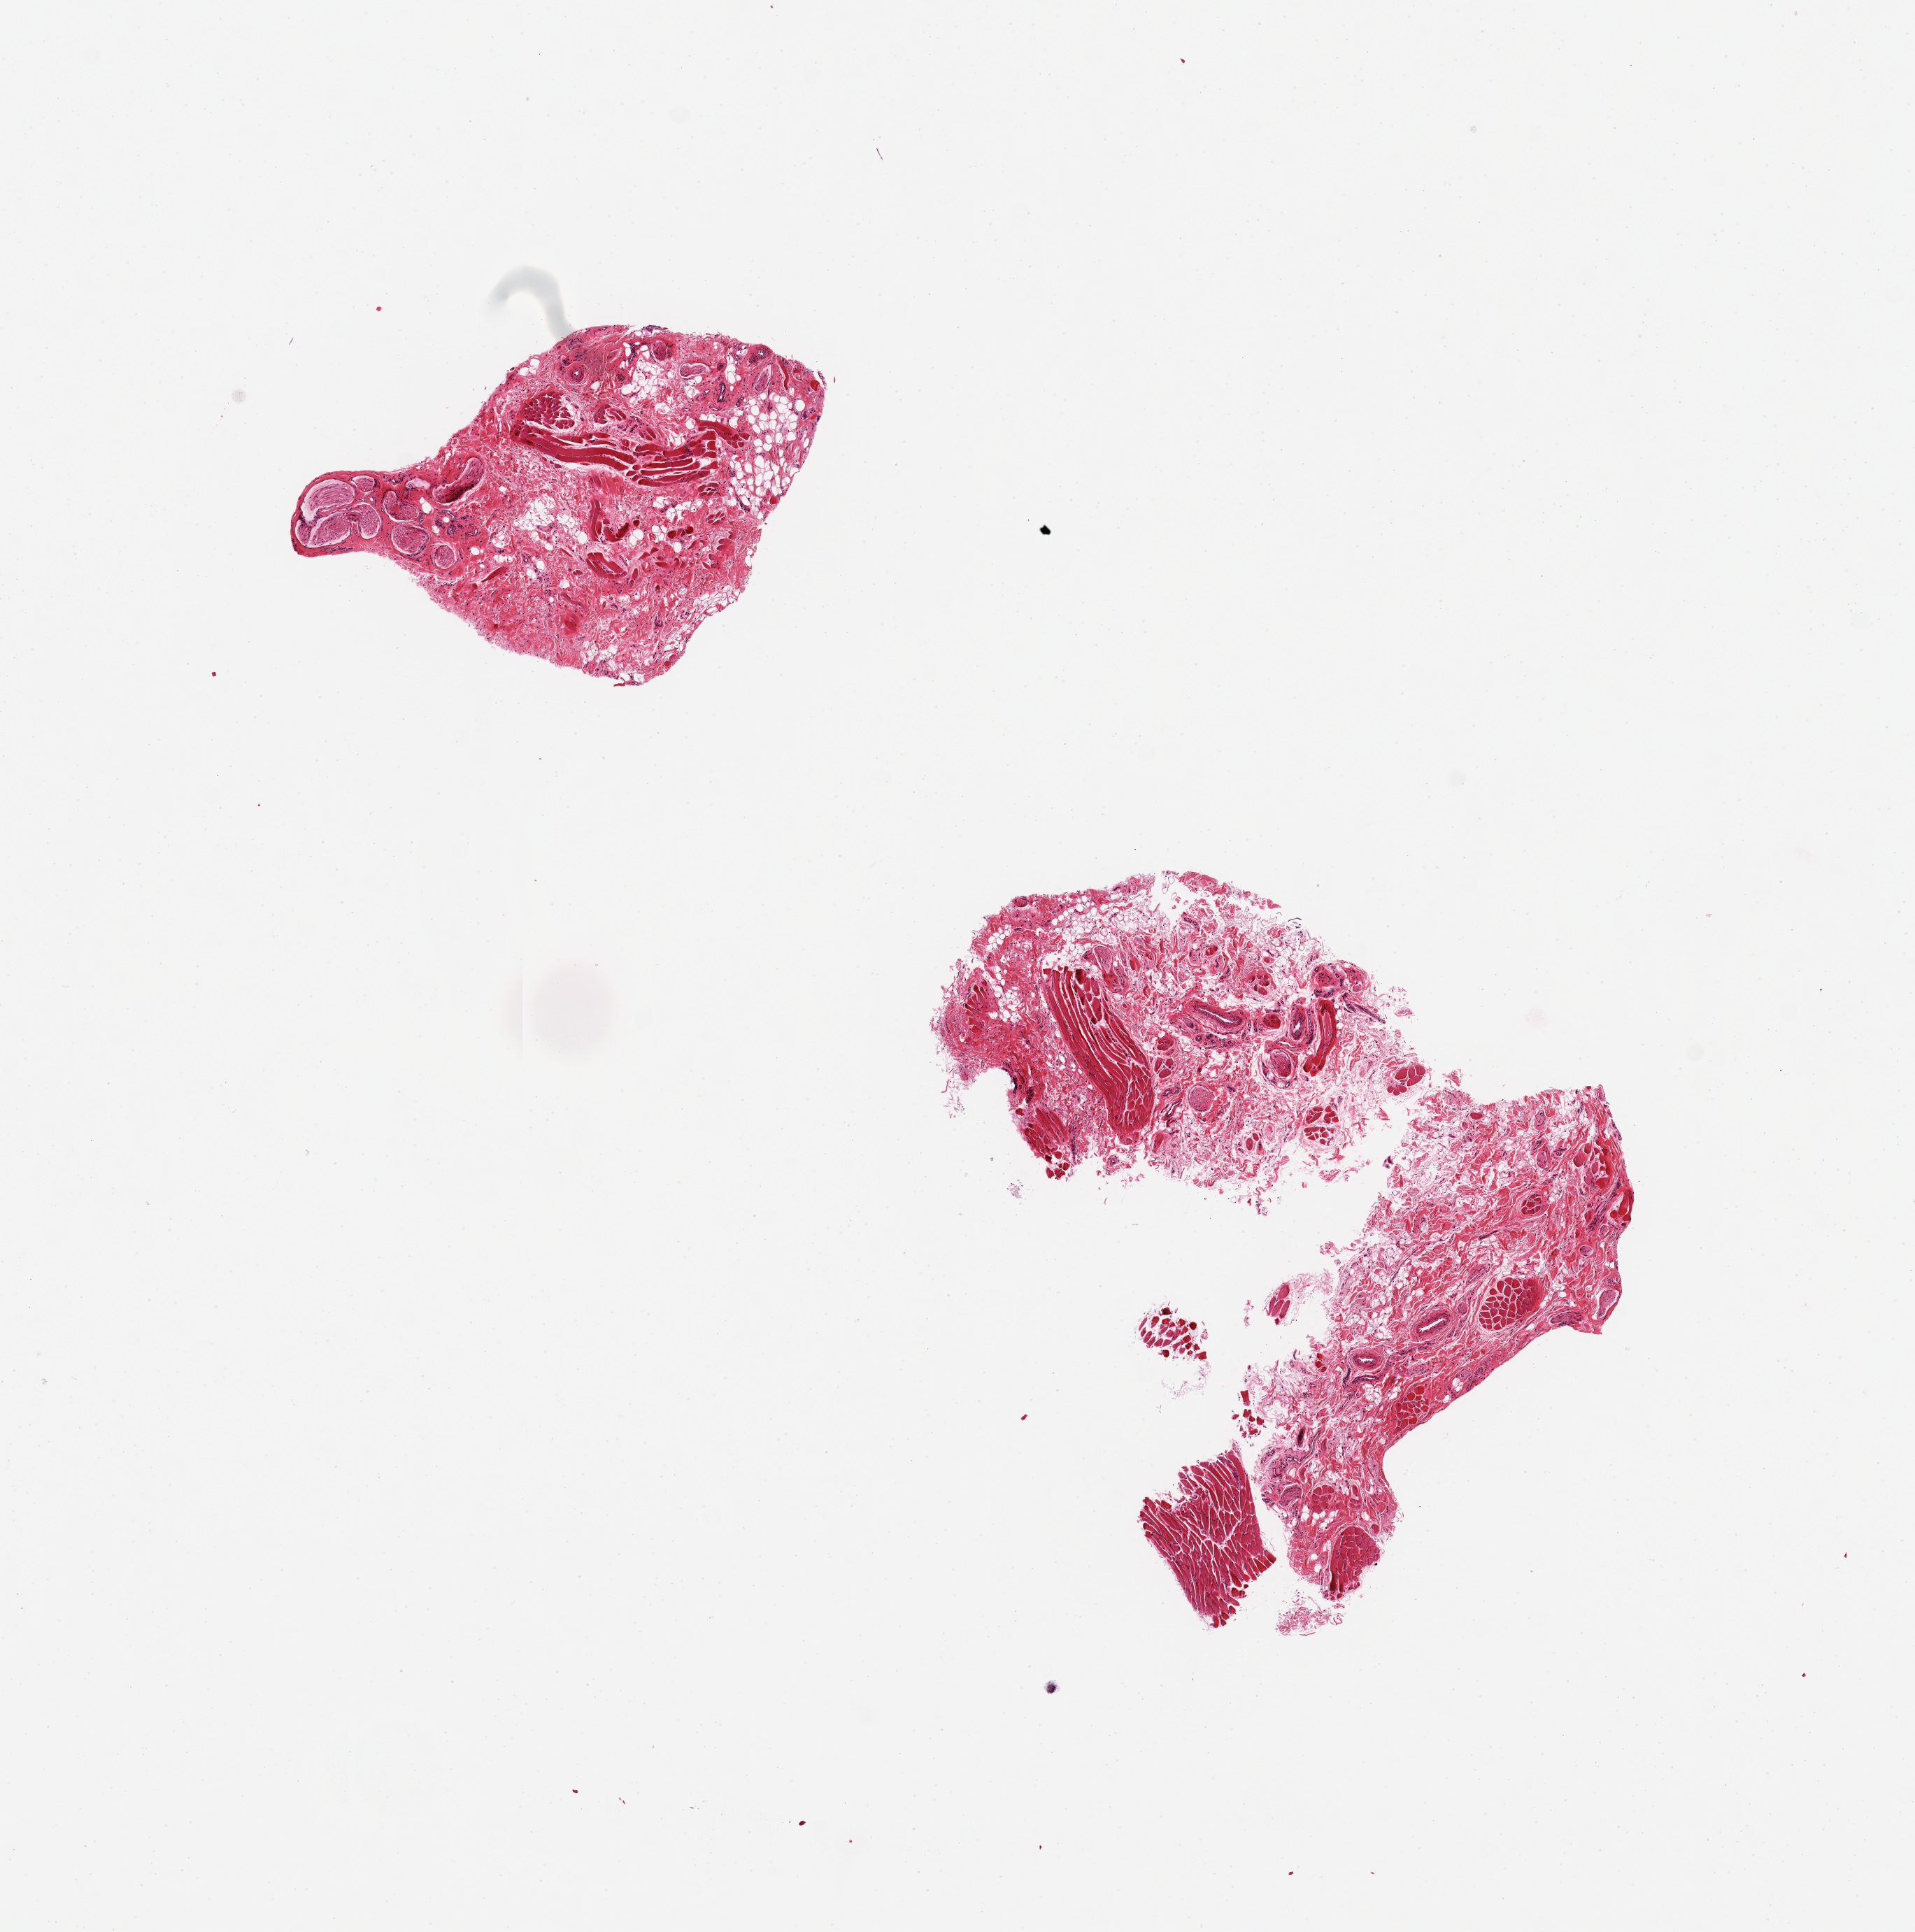
Whole-slide image, H&E stain — low-resolution overview of the scanned area, about 10.8 x 10.9 mm; PAXgene-fixed, paraffin-embedded tissue; sampled site (target tissue): minor salivary gland; donor tissue sample. Donor: male.
- reviewer comment on this tissue sample: 2 pieces; nerve/stroma/skeletal muscle, no salivary gland elements